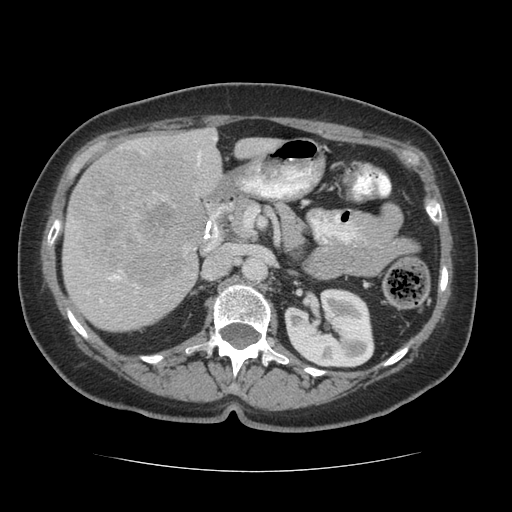
Contrast-enhanced abdominal CT (liver protocol), one axial slice. Position 28 of 75 along the scan axis. Reconstruction kernel STANDARD. 140 kVp. Soft-tissue window (W 400 / L 40 HU). 512 × 512 image matrix, field of view 360 × 360 mm. From the clinical record (not read from this slice): diagnosis: hepatocellular carcinoma (patient treated with transarterial chemoembolisation; whether this scan precedes or follows treatment is not stated here); TNM stage (as recorded): Stage-I; Child-Pugh class: A; tumour nodularity: uninodular.
Structures marked on this image (semi-automatic segmentation, software-assisted and operator-edited):
- liver parenchyma outside the tumour (the mass and vessels are separate outlines, so this box may not span the whole liver): bounding box [x1, y1, x2, y2] px = [62, 128, 280, 330]
- mass: [68, 147, 208, 290]
- liver vessels: [67, 137, 217, 303]